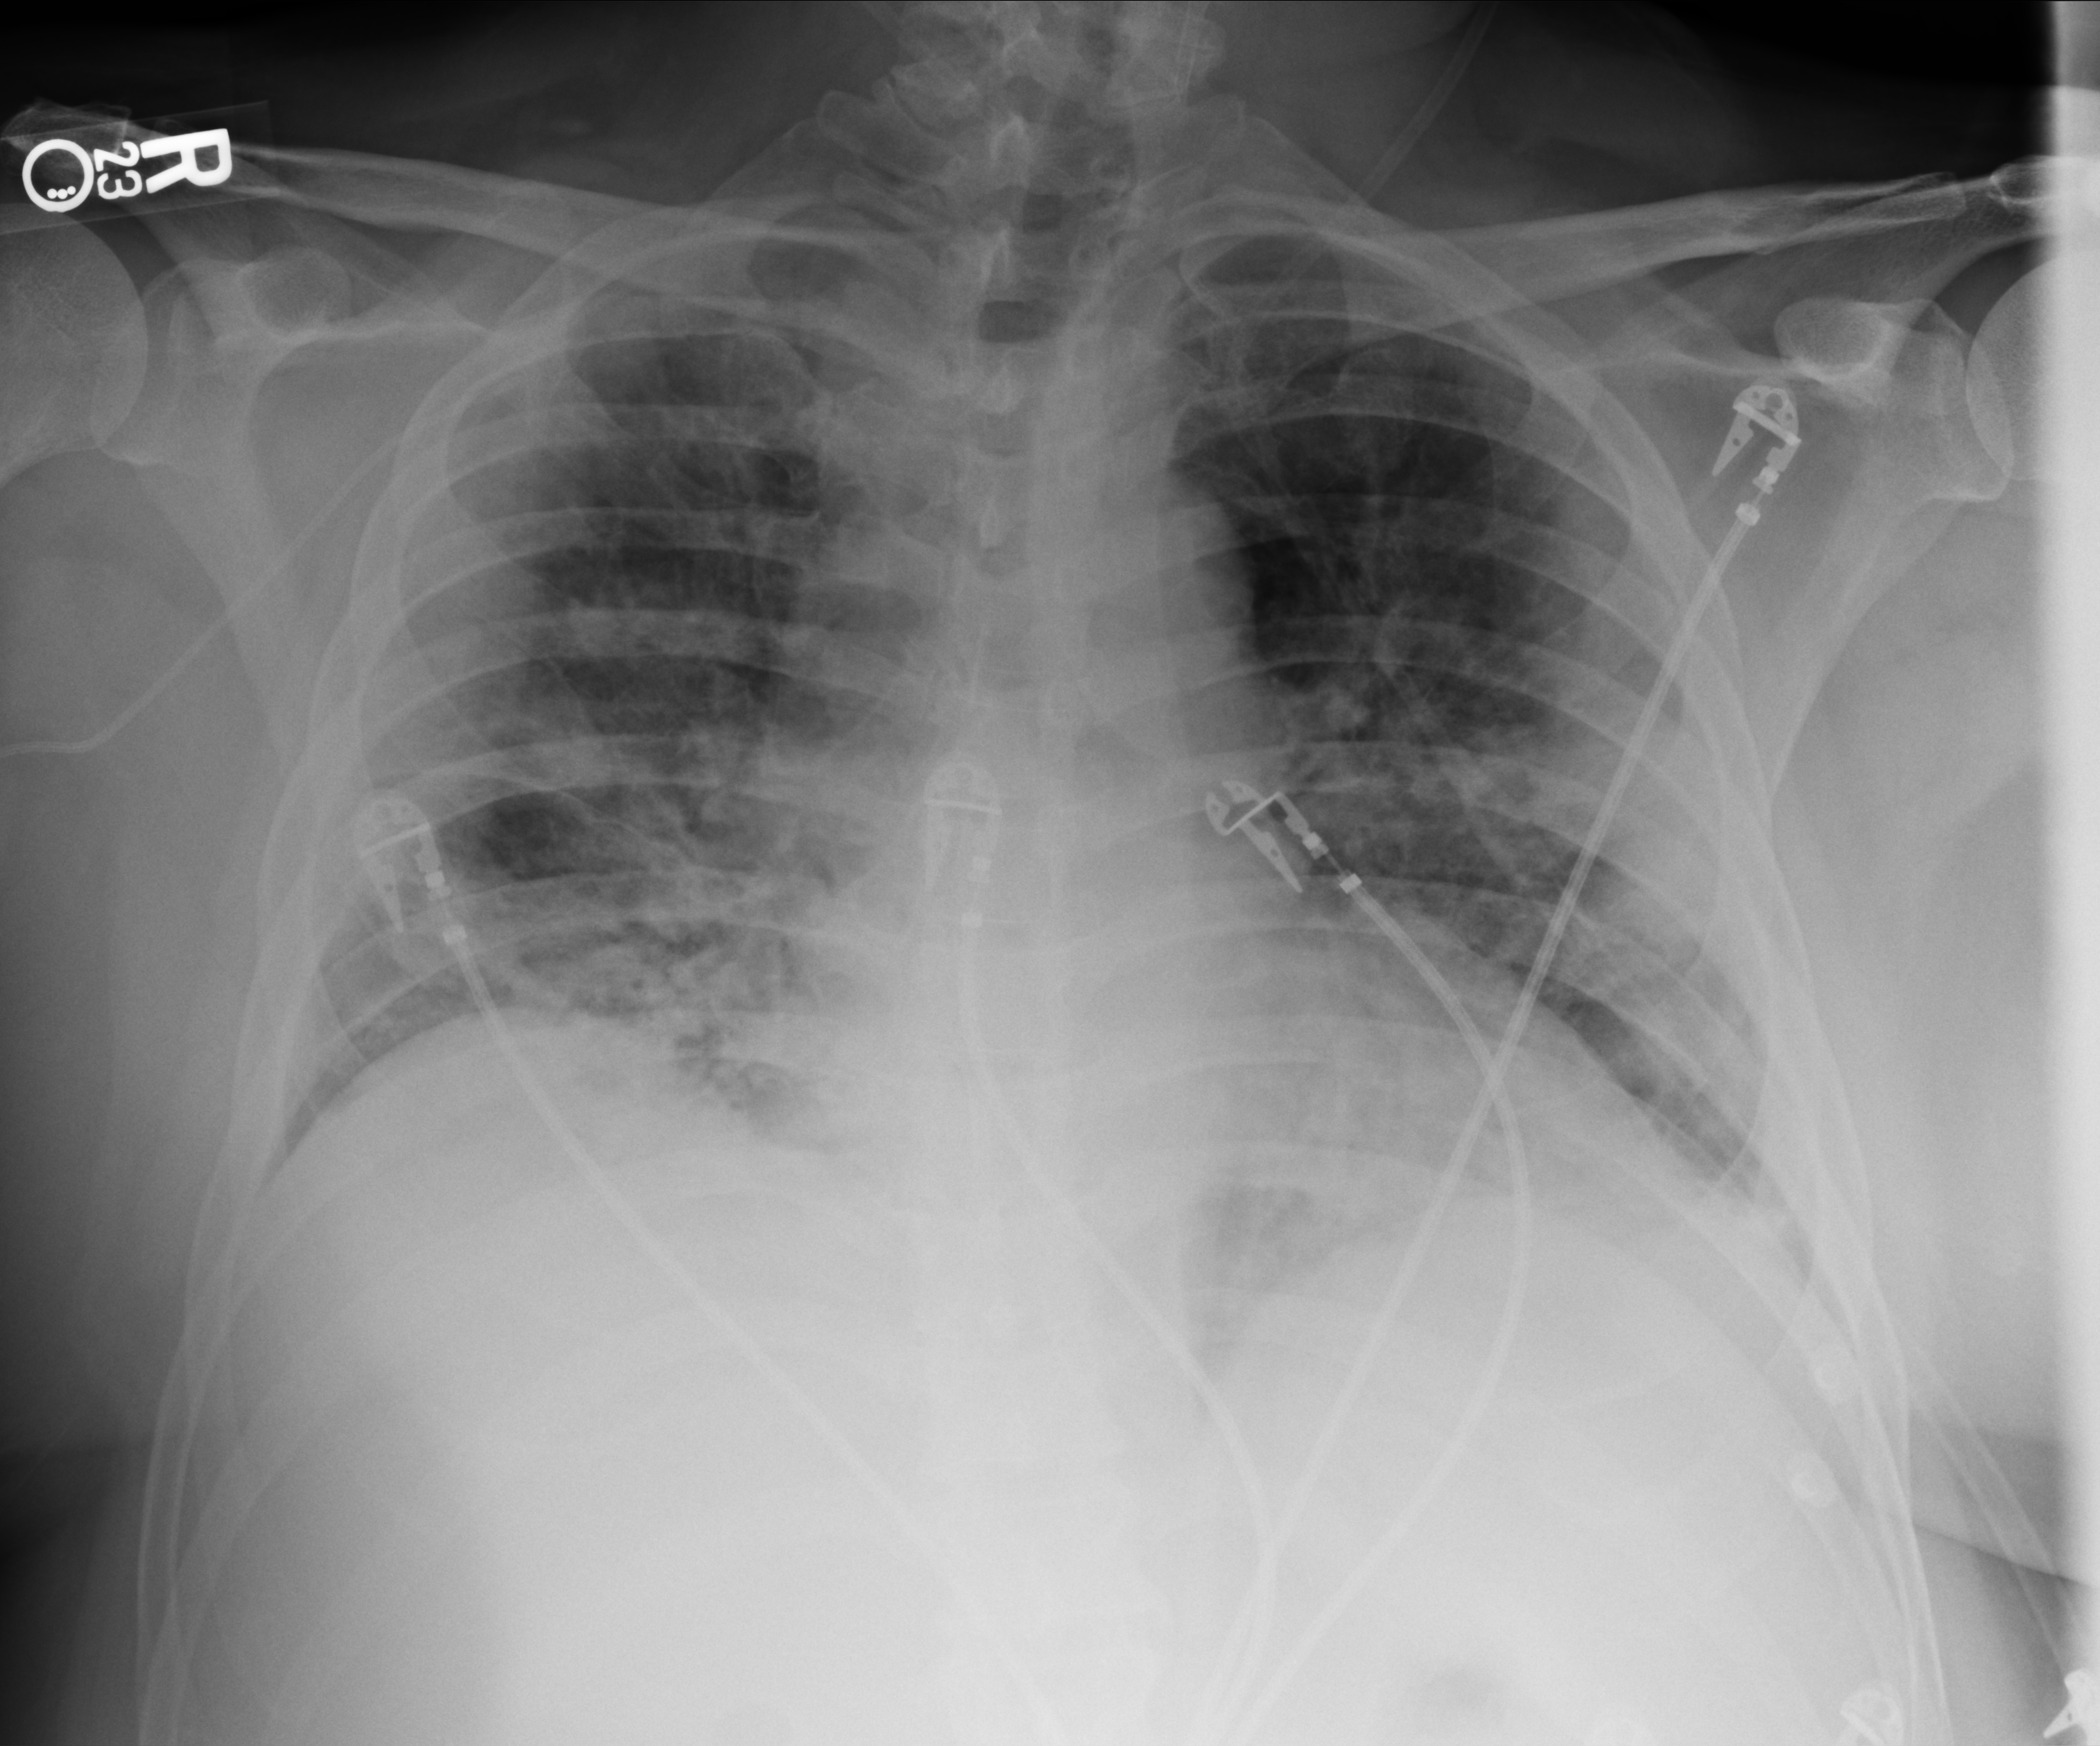
Portable chest radiograph; anteroposterior (AP) projection. Male patient hospitalised with COVID-19, age 60–74 years.
From the hospital-stay record, not from the radiograph (when in the stay this image was taken is not recorded): admitted to intensive care during this hospital stay: no.